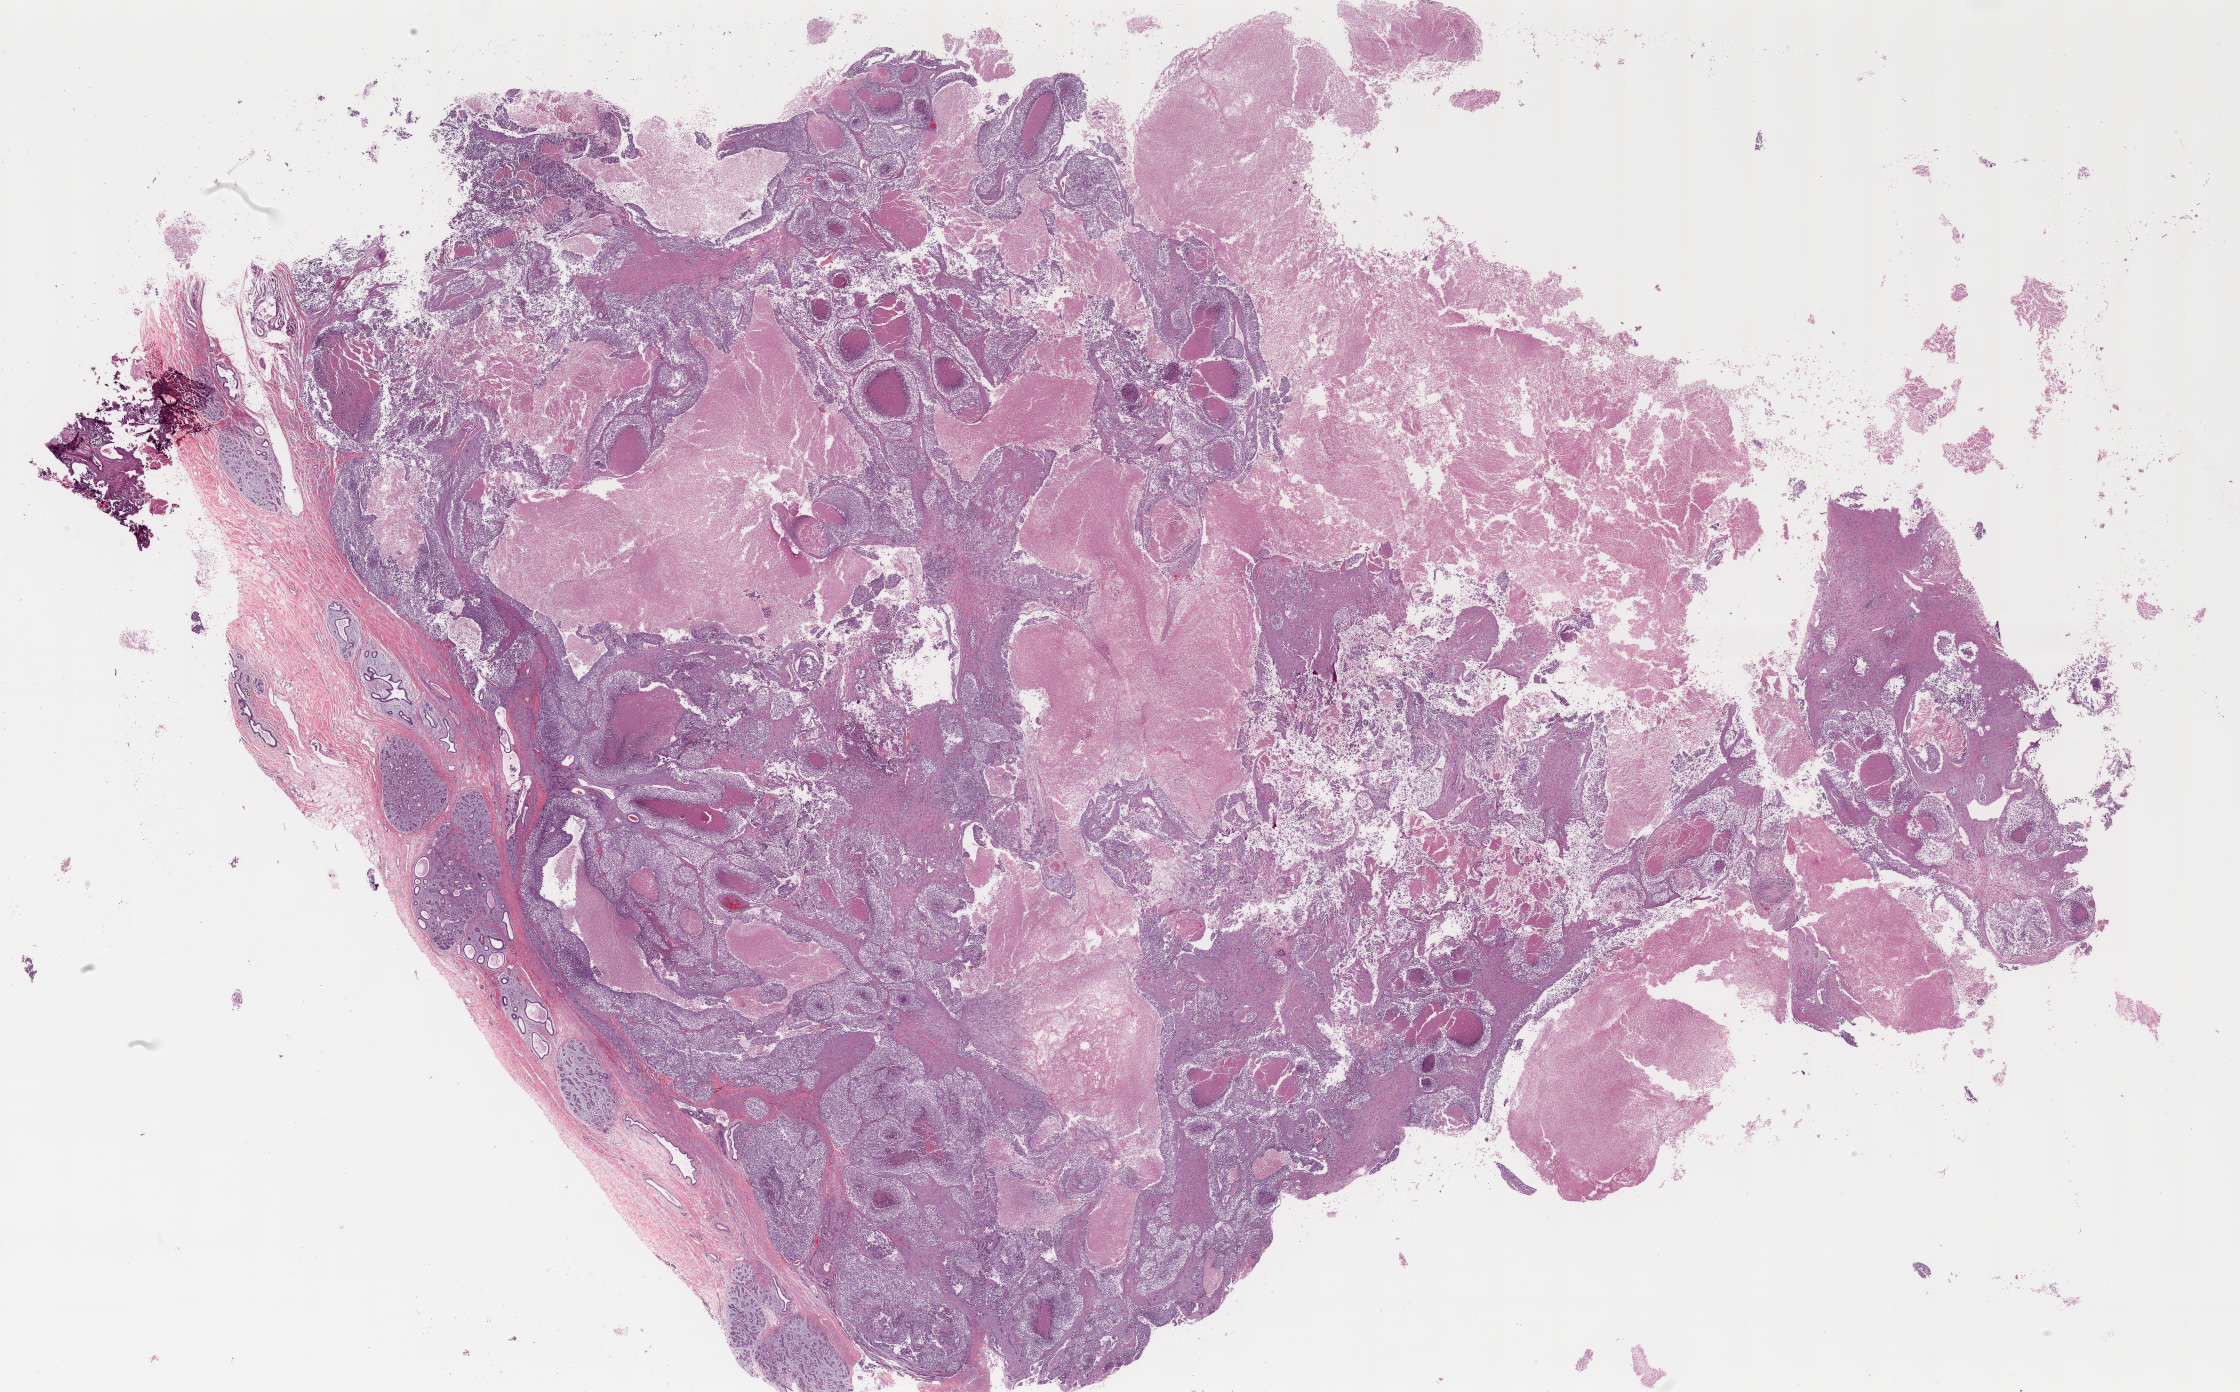
Digitized H&E tissue section (whole slide), shown as a low-resolution overview of the whole scanned area (about 35.8 x 22.2 mm). FFPE section. Sample: primary tumour, breast. Female, age 36 years at initial diagnosis.
Lymph nodes positive (case pathology): 0 of 17 examined. Pathologic diagnosis: Infiltrating duct carcinoma, NOS. AJCC pathologic stage: IIA (6th edition).